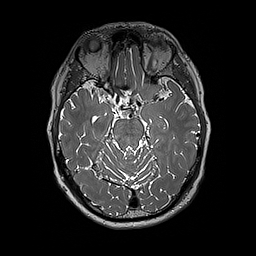
Brain MRI from a brain-tumour surgery series, one axial slice. Slice 121 of 192 in the series (ordered by position). 256 × 256 image matrix. From the clinical record (not read from this slice): histopathology: Glioblastoma; WHO grade: 4; IDH mutation: no.
Annotated regions visible in this slice (outlined manually by an expert reader):
- tumour: bounding box [x1, y1, x2, y2] px = [142, 87, 150, 100]